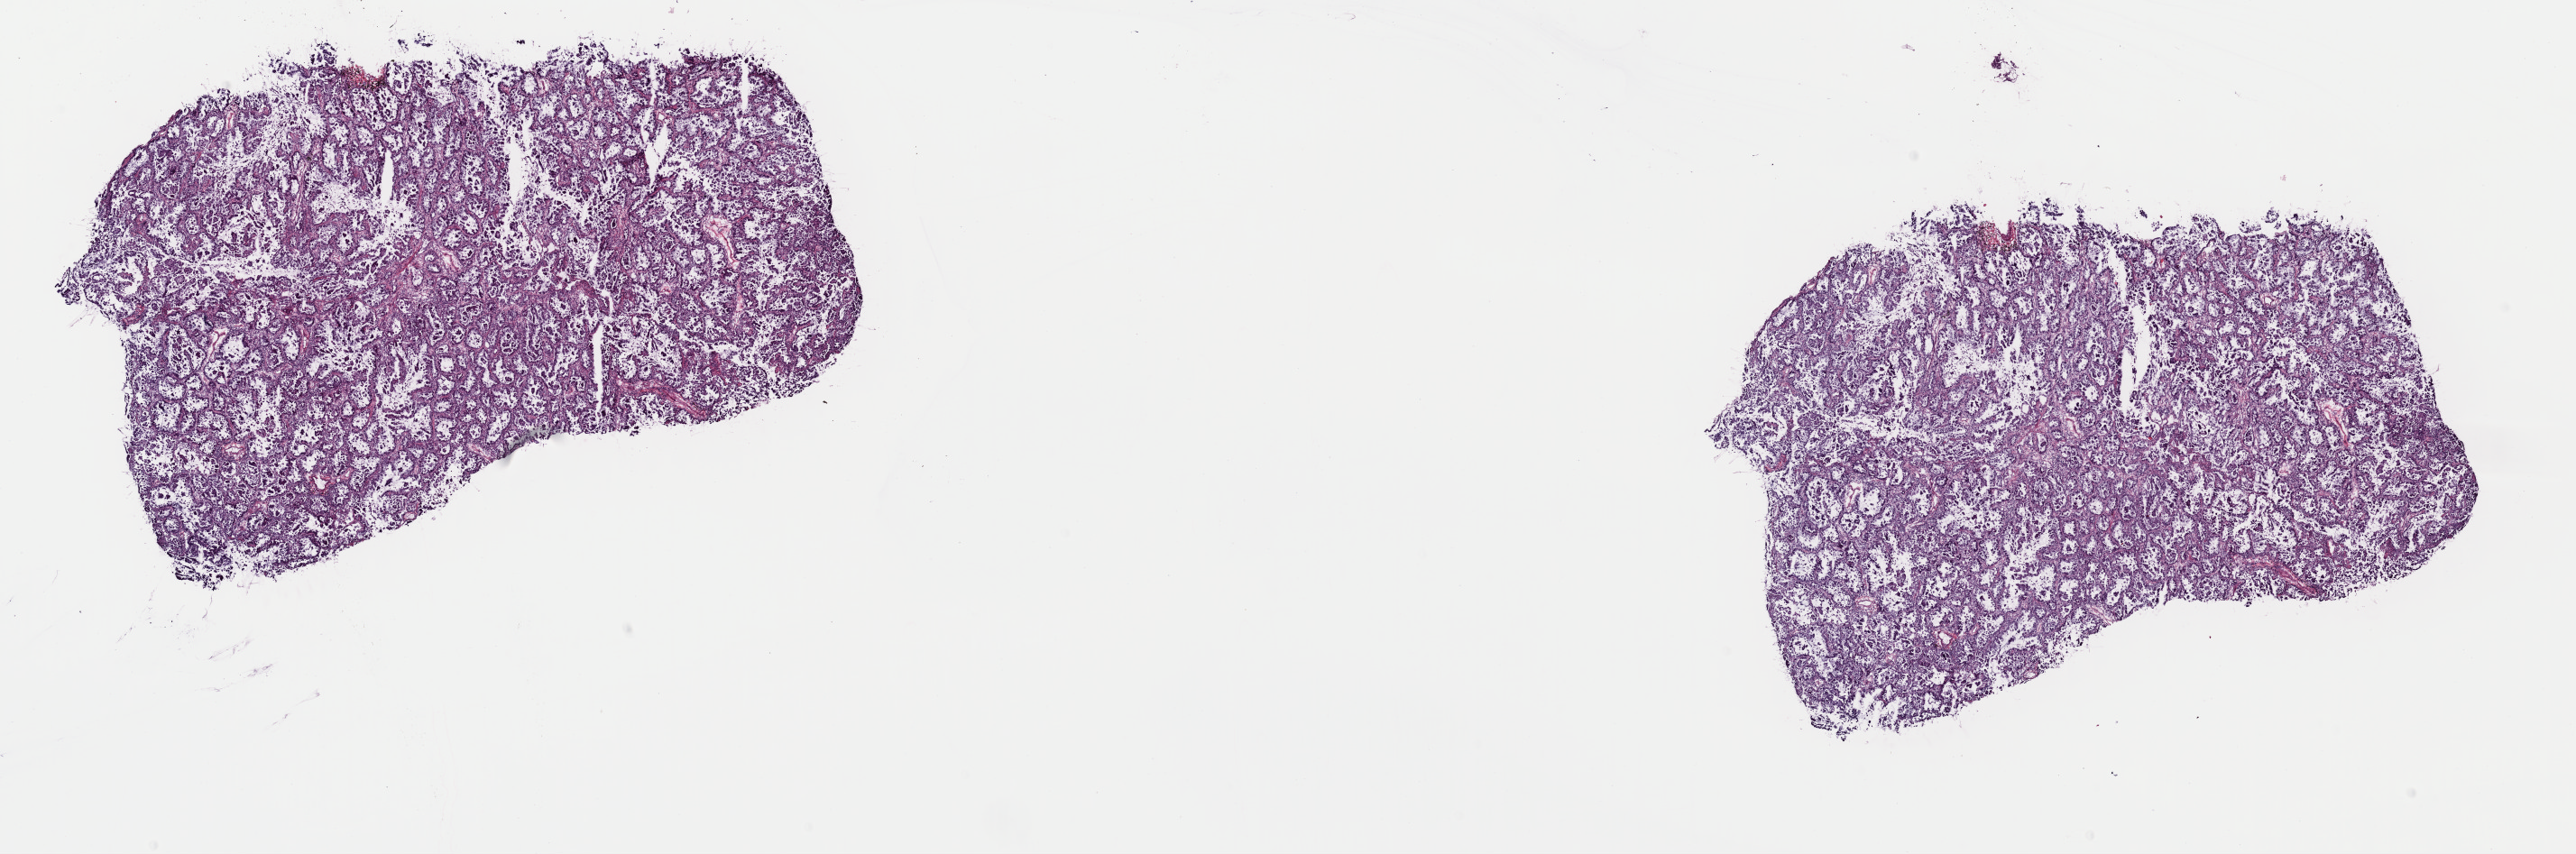
Digitized H&E-stained tissue section (whole slide), shown as a low-resolution overview of the whole scanned area (about 22.6 x 7.5 mm). Frozen section from the top of the tissue portion. Primary tumour sample from the lung. Female, age 70 years at initial diagnosis. Pathologist review of this section (percent, as recorded): tumour cells 100%, tumour nuclei 75%, normal cells 0%, stromal cells 0%, necrosis 0%. Infiltration values recorded for this section: lymphocyte infiltration 2%, monocyte infiltration 4%, neutrophil infiltration 0%.
* TNM: T2 N2 M0
* histologic diagnosis: Adenocarcinoma with mixed subtypes
* laterality: right
* AJCC pathologic stage: IIIA (6th edition)